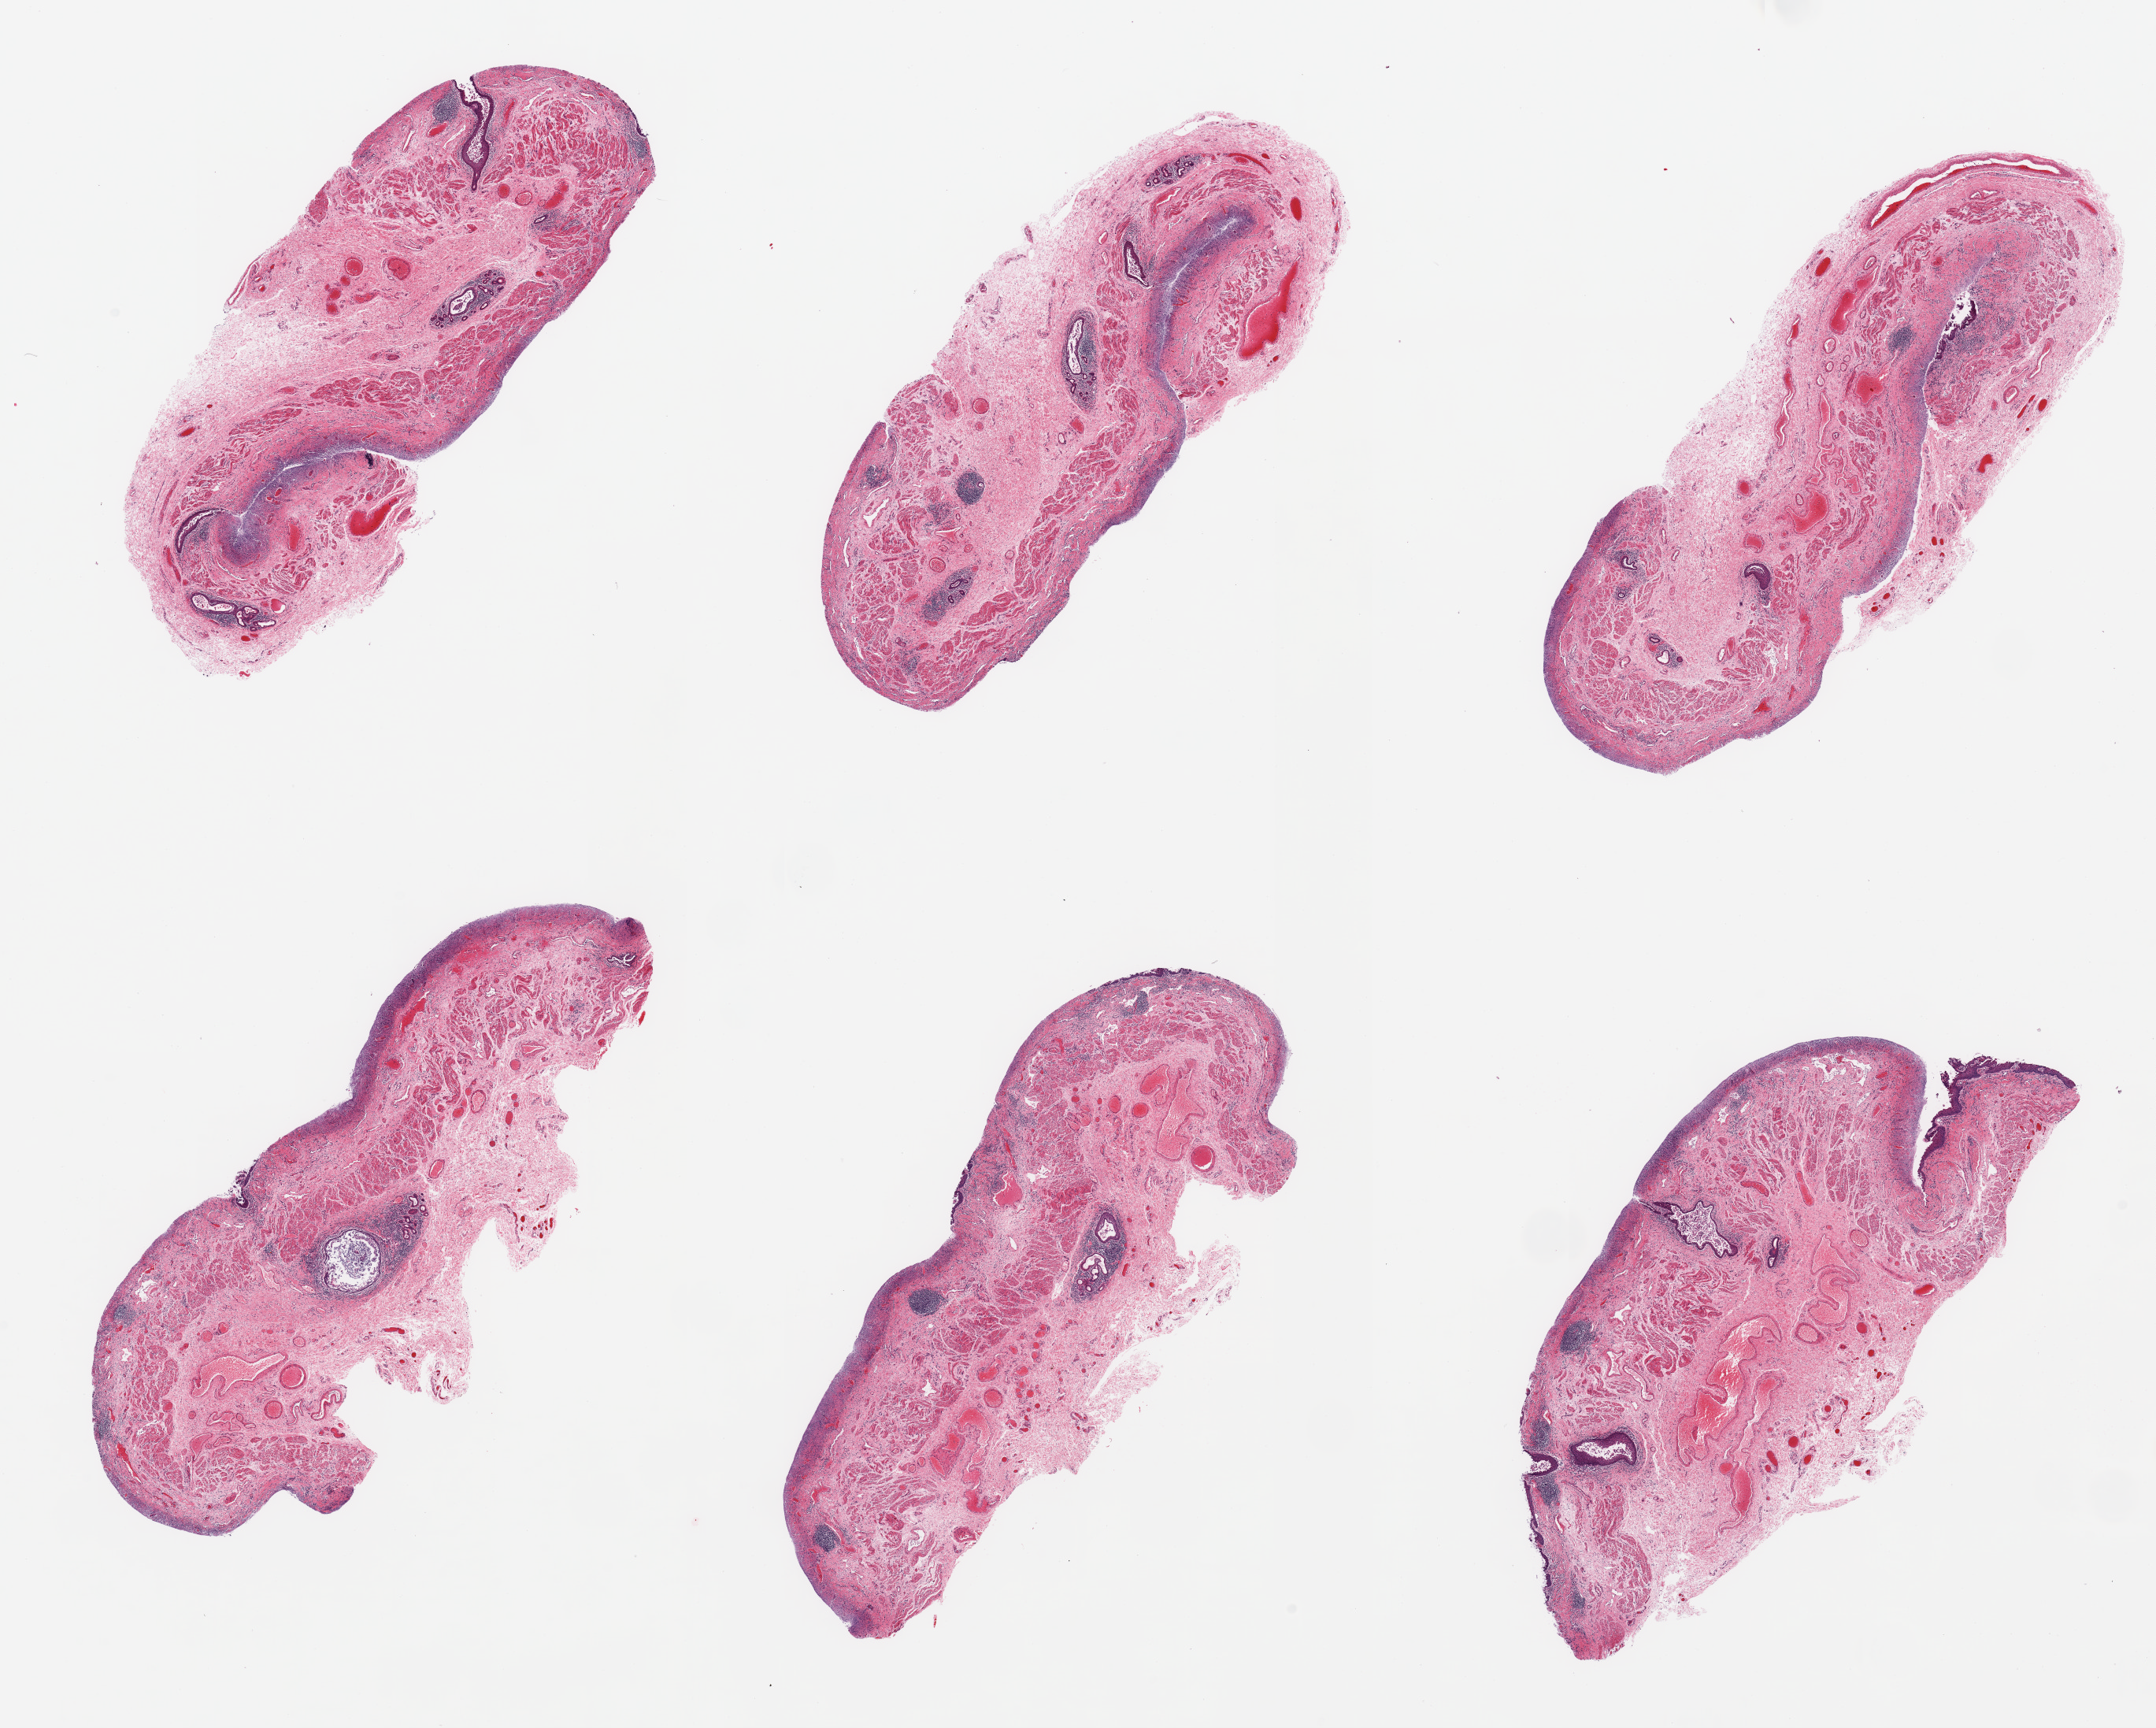
Whole-slide image, haematoxylin and eosin stain, low-resolution overview of the scanned area, about 21.7 x 17.4 mm, PAXgene-fixed, paraffin-embedded tissue, sampled site (target tissue): esophageal mucous membrane, donor tissue sample.
Pathologist's review note for this sample: 6 pieces, mucosa extensively sloughed; erosive esophagitis.